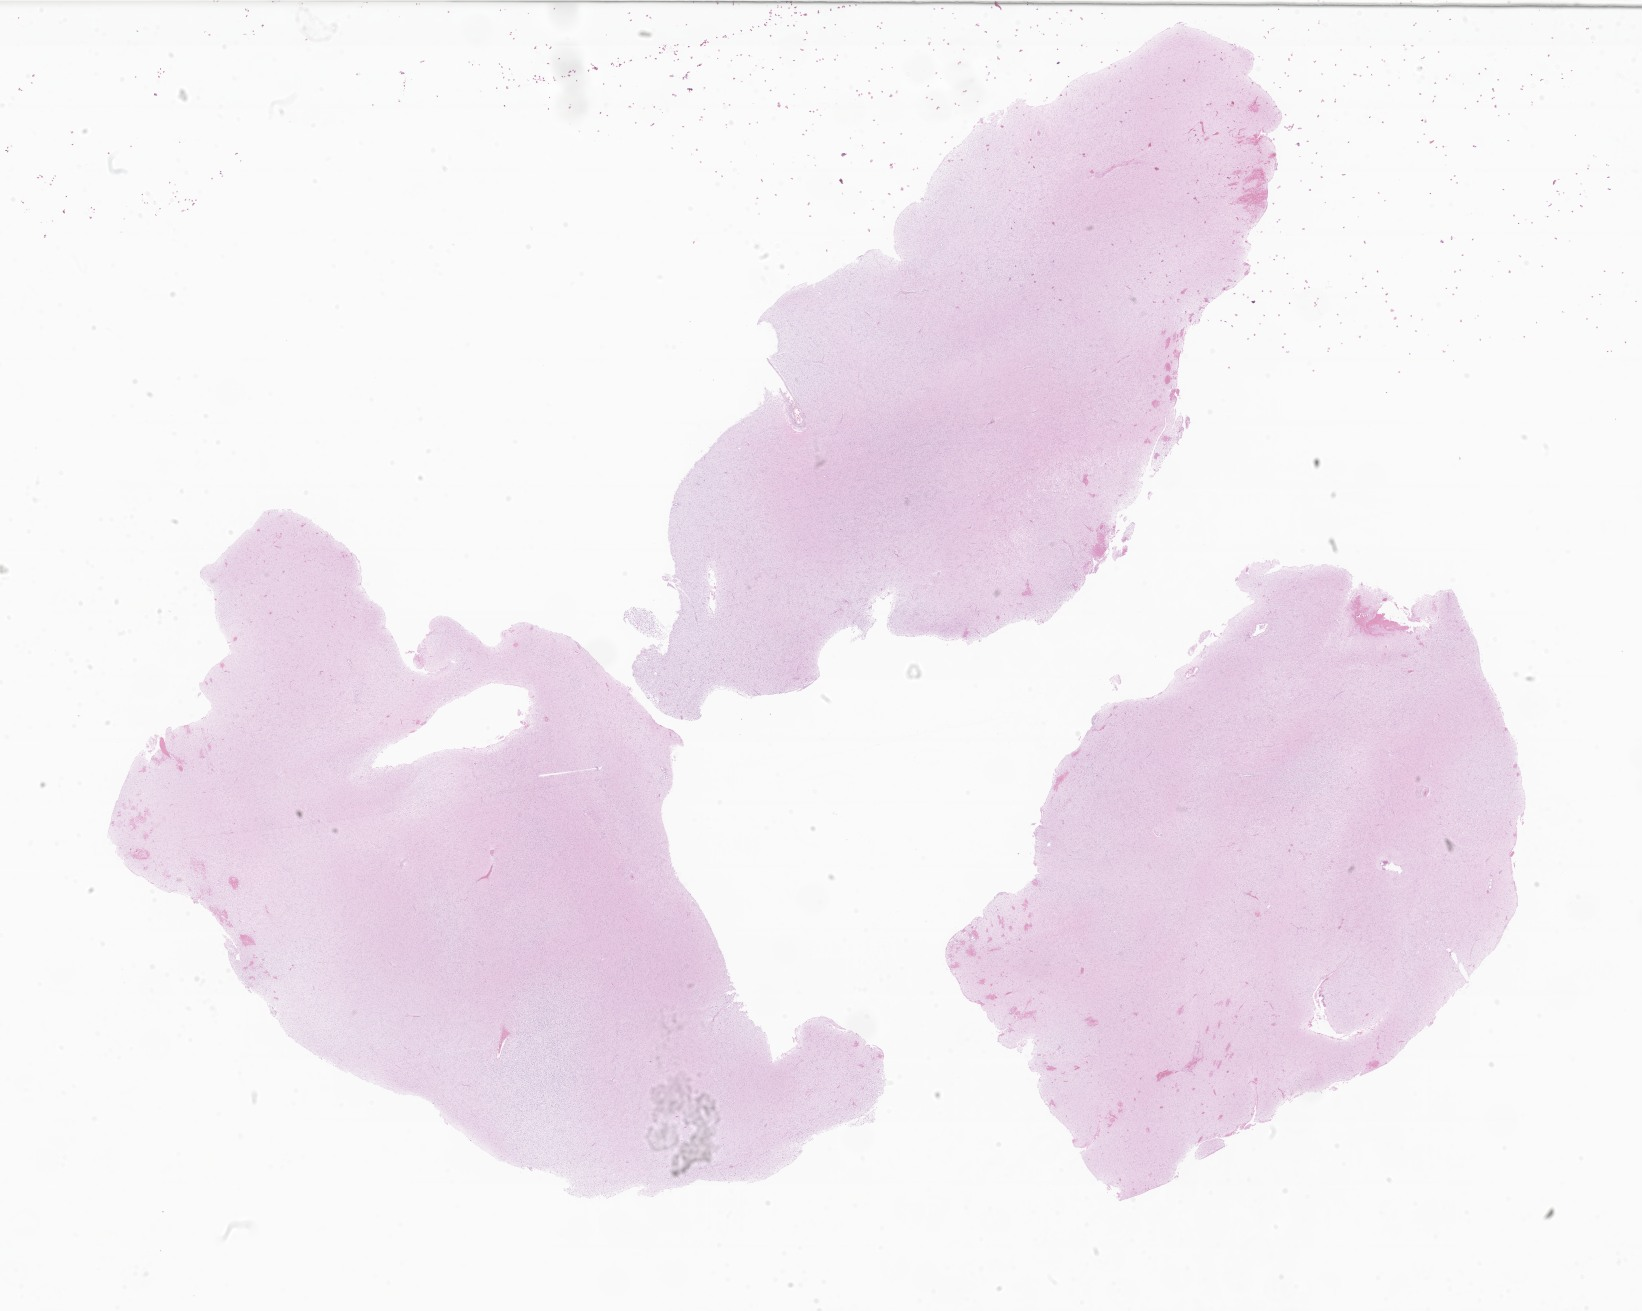
Hematoxylin and eosin (H&E) whole-slide image of tumor tissue from the brain, shown as a low-resolution overview of the whole scanned area (about 27.7 x 22.1 mm); formalin-fixed paraffin-embedded section. Female patient, age 162 months (13 years 6 months).
* diagnosis: Pilocytic astrocytoma